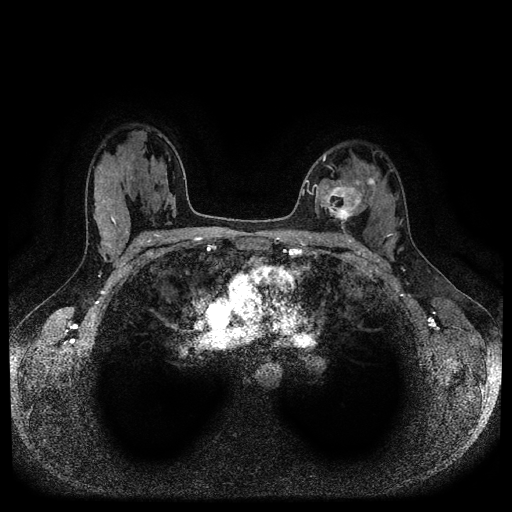
Breast MRI (dynamic contrast-enhanced, multi-phase), one axial slice. Slice 65 of 116 in the series (ordered by position). Dynamic contrast-enhanced series, time point 2 of 5 at this slice position (early post-contrast). 1.5 T. TE 2.6 ms, TR 5.3 ms. 2 mm slice thickness. 512 × 512 image matrix, field of view 350 × 350 mm. Female patient, age 33 years.
Outlined on this slice (semi-automatic segmentation, software-assisted and operator-edited):
- breast lesion (labelled 'tumour' in the annotation; benign lesions carry a separate 'benign' label): box from (x=319, y=184) to (x=364, y=222) px